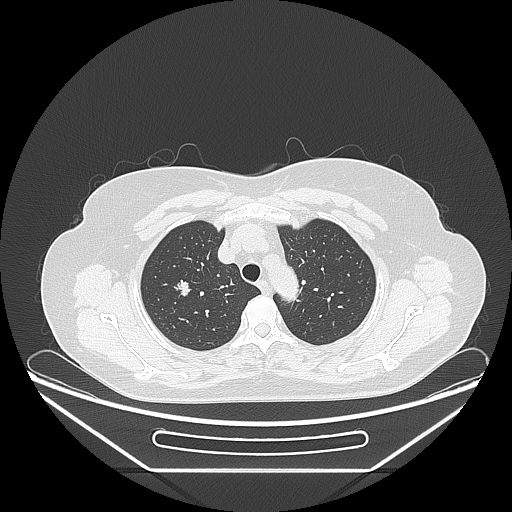
Chest CT, one axial slice. 120 kVp. Lung window (W 1500 / L -600 HU). 512 × 512 image matrix, field of view 433 × 433 mm. Female patient, age 60 years. Case-level facts recorded for this patient, not image findings: clinical TNM (as recorded): T1c N0 M0; histopathological grade: G2-3.
Structures marked on this image (rectangle marked by the reading radiologist):
- lung tumour (recorded histology: adenocarcinoma): bounding box <175,275,192,302> (left, top, right, bottom; pixels)